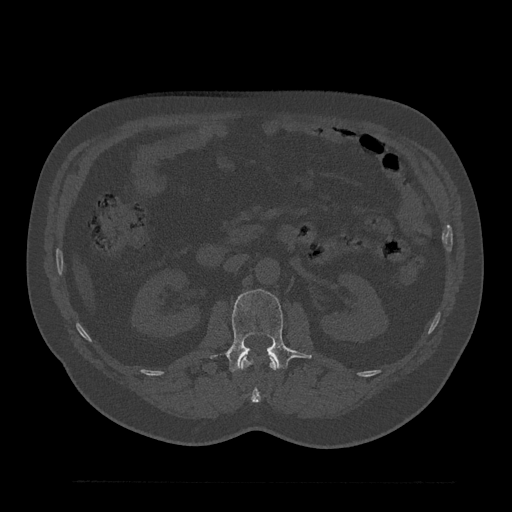
CT including the spine, one axial slice. Position 116 of 797 along the scan axis. Reconstruction kernel Br40s/3. 120 kVp. Bone window (W 1800 / L 400 HU). 0.5 mm slice thickness. 512 × 512 image matrix. Male patient, age 61 years. Case-level facts recorded for this patient, not image findings: primary cancer: prostate.
Outlined on this slice (semi-automatically segmented with operator editing):
- L1 vertebra: bounding box (x1, y1, x2, y2) in pixels: (241, 353, 277, 403)
- L2 vertebra: (227, 289, 311, 372)